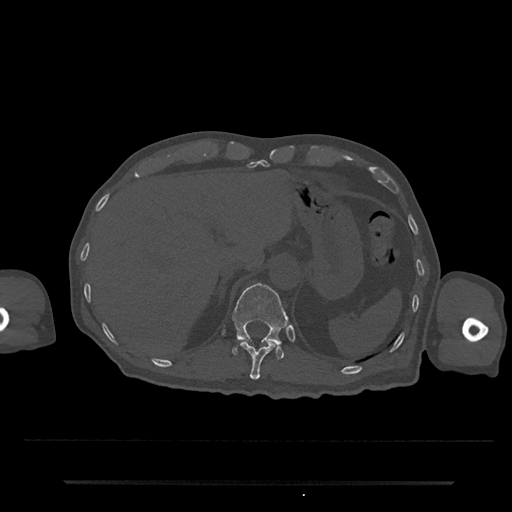
CT including the spine, one axial slice; slice 223 of 797 in the series (ordered by position); bone window (W 1800 / L 400 HU); 0.5 mm slice thickness; 512 × 512 image matrix, field of view 427 × 427 mm. Male patient, age 74 years. Case-level facts recorded for this patient, not image findings: primary cancer: prostate.
Outlined on this slice (semi-automatically segmented with operator editing):
- T11 vertebra: bounding box [x1, y1, x2, y2] px = [238, 340, 277, 380]
- T12 vertebra: [232, 283, 288, 359]